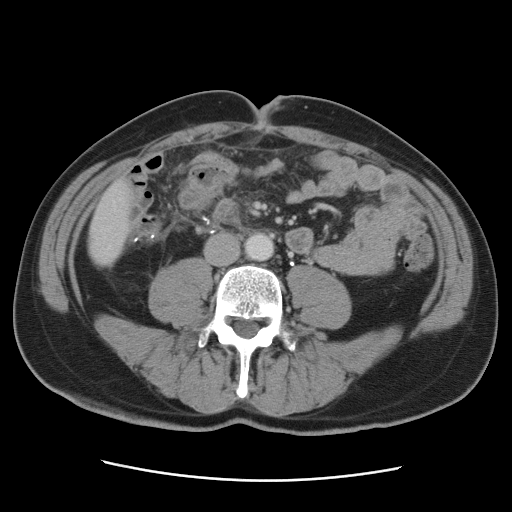
Contrast-enhanced abdominal CT, one axial slice. Slice 8 of 89 in the series (ordered by position). 120 kVp. Intravenous contrast given. Soft-tissue window (W 400 / L 40 HU). 5 mm slice thickness. 512 × 512 image matrix, field of view 366 × 366 mm. Male patient, age 59 years. Case-level facts recorded for this patient, not image findings: diagnosis: colorectal cancer liver metastases, imaged before liver resection; multiple liver metastases: yes; largest metastasis: 0.6 cm; disease in both lobes: yes.
Outlined on this slice (outlined manually by an expert reader):
- liver: bounding box <90,183,131,265> (left, top, right, bottom; pixels)
- planned liver remnant (the part of the liver to remain after resection): <89,183,131,259>